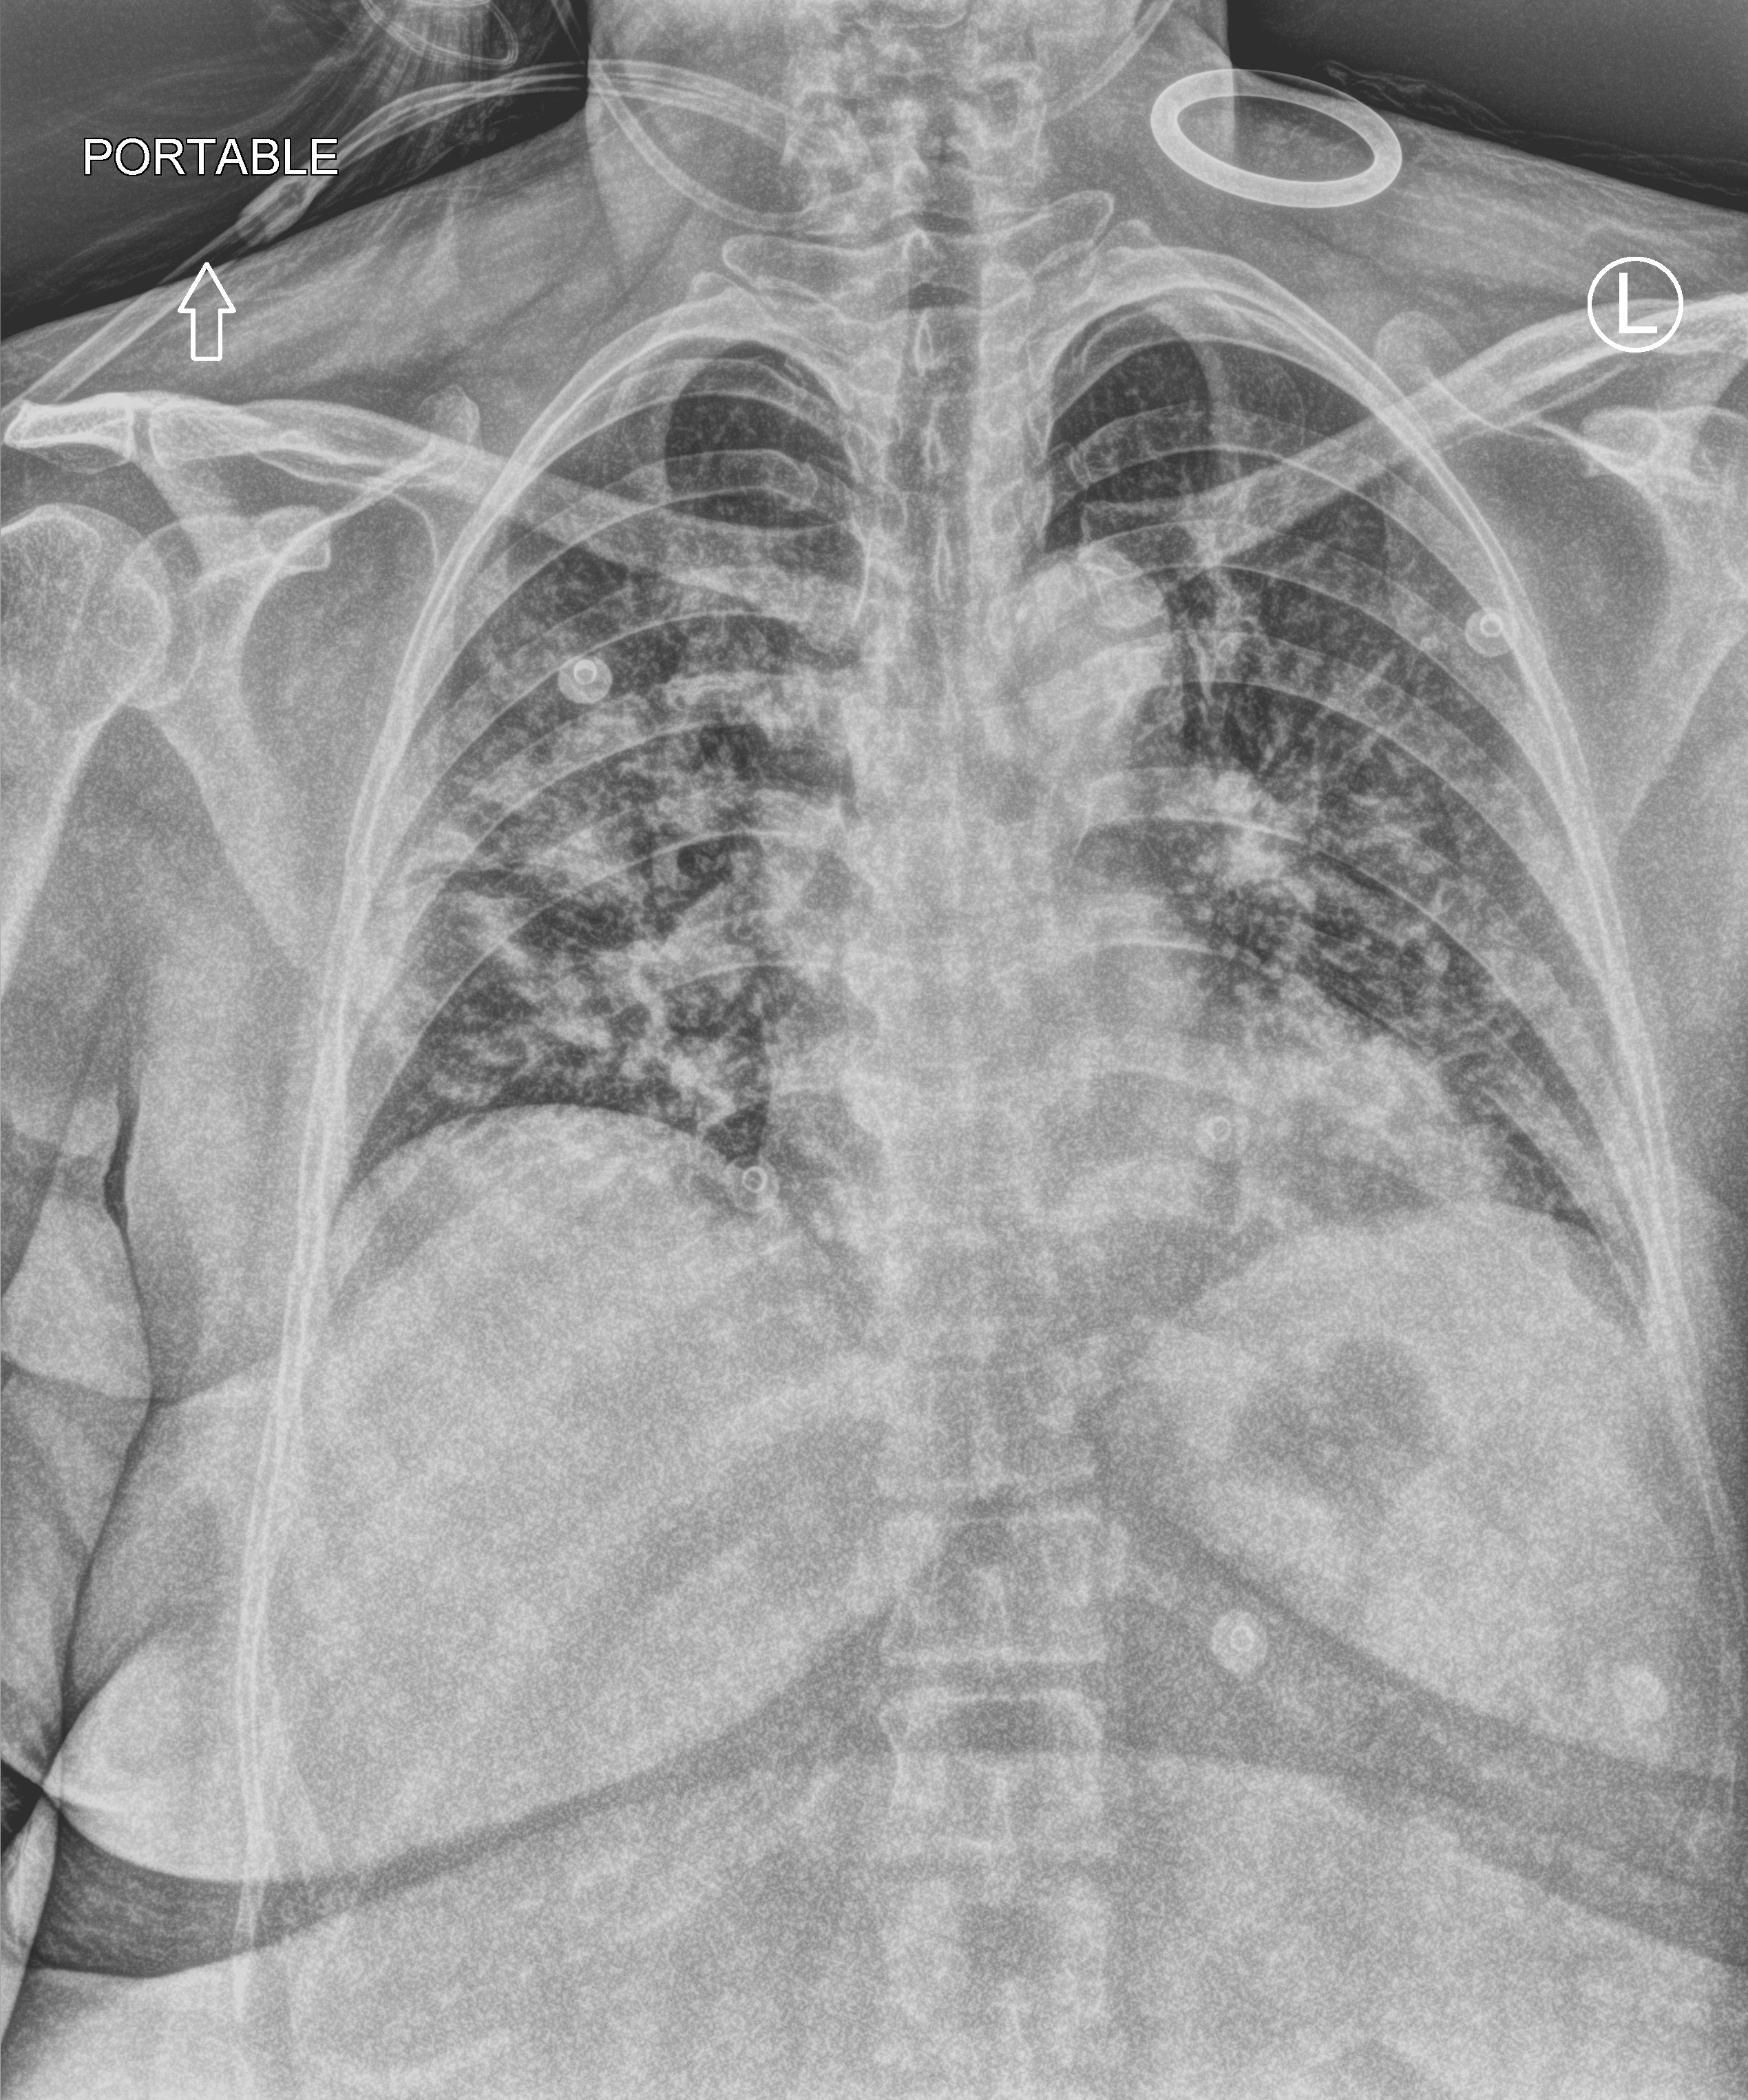
Portable chest radiograph; anteroposterior (AP) projection. Patient hospitalised with COVID-19; female, aged 18–59 years.
Hospital-stay facts (about this admission, not read from this image; timing relative to this image not recorded): chronic kidney disease (admission record): no.